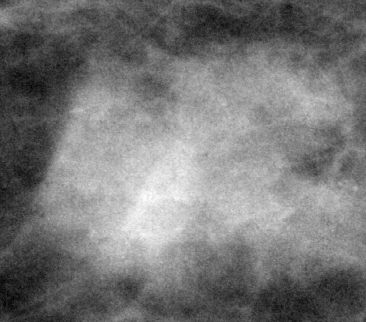
Crop from a digitized film mammogram around one marked abnormality, right breast, CC view, BI-RADS breast density category 2 (scale 1–4).
Finding: mass, shape irregular, margins spiculated; BI-RADS assessment category 5; pathology result (as recorded, not read from the image): malignant.